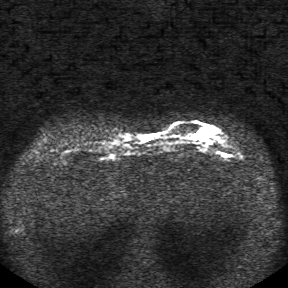
Breast MRI, one axial slice; position 7 of 34 along the scan axis; diffusion-weighted series; image 2 of 4 stored at this slice position (different b-values; order by instance number); 1.5 T; 5 mm slice thickness; 288 × 288 image matrix, field of view 340 × 340 mm. Female patient.
Annotated regions visible in this slice (outlined manually by an expert reader):
- tumour on diffusion-weighted imaging: bounding box <196,124,219,139> (left, top, right, bottom; pixels)